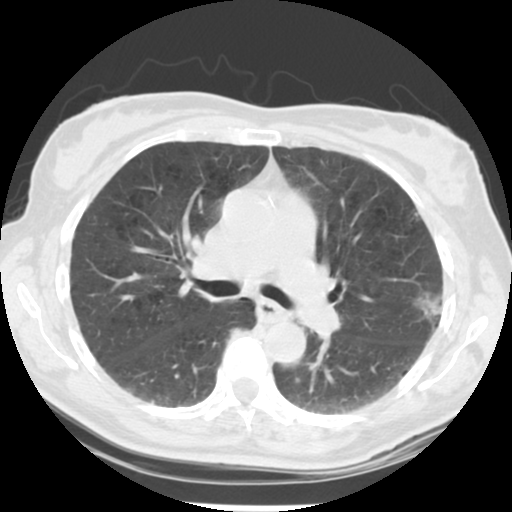
Chest CT (low-dose screening protocol), one axial image, second annual screen, lung window (W 1500 / L -600 HU), 2.5 mm slice thickness, standard (soft-tissue) reconstruction kernel (STANDARD). Female participant, aged 61 years at enrolment. Current smoker at enrolment.
Expert reader's lesion annotation, box from (x=405, y=279) to (x=464, y=340) px. The exam's reader record, not a measurement of the box and not confirmed to be the same lesion: non-calcified nodule or mass ≥4 mm, left upper lobe, 15 × 15 mm, poorly defined margins, mixed attenuation, pre-existing on the prior screen: no. Lung cancer was diagnosed 152 days after this screen: bronchiolo-alveolar adenocarcinoma, NOS, left upper lobe, well differentiated (G1), stage IA (AJCC 6th edition), 11 mm at pathology.